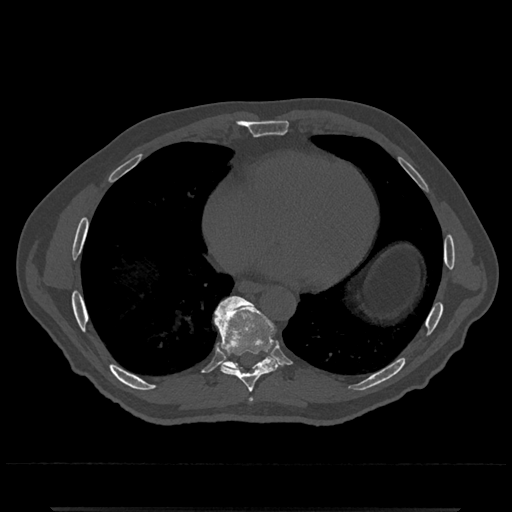
CT including the spine, one axial slice. Slice 650 of 797 in the series (ordered by position). Reconstruction kernel Br40s/3. Bone window (W 1800 / L 400 HU). 0.5 mm slice thickness. 512 × 512 image matrix. Patient: male, 67 years. From the clinical record (not read from this slice): primary cancer: prostate.
Annotated regions visible in this slice (semi-automatic segmentation, software-assisted and operator-edited):
- T8 vertebra: bounding box [x1, y1, x2, y2] px = [216, 299, 279, 392]
- T9 vertebra: [213, 295, 277, 371]